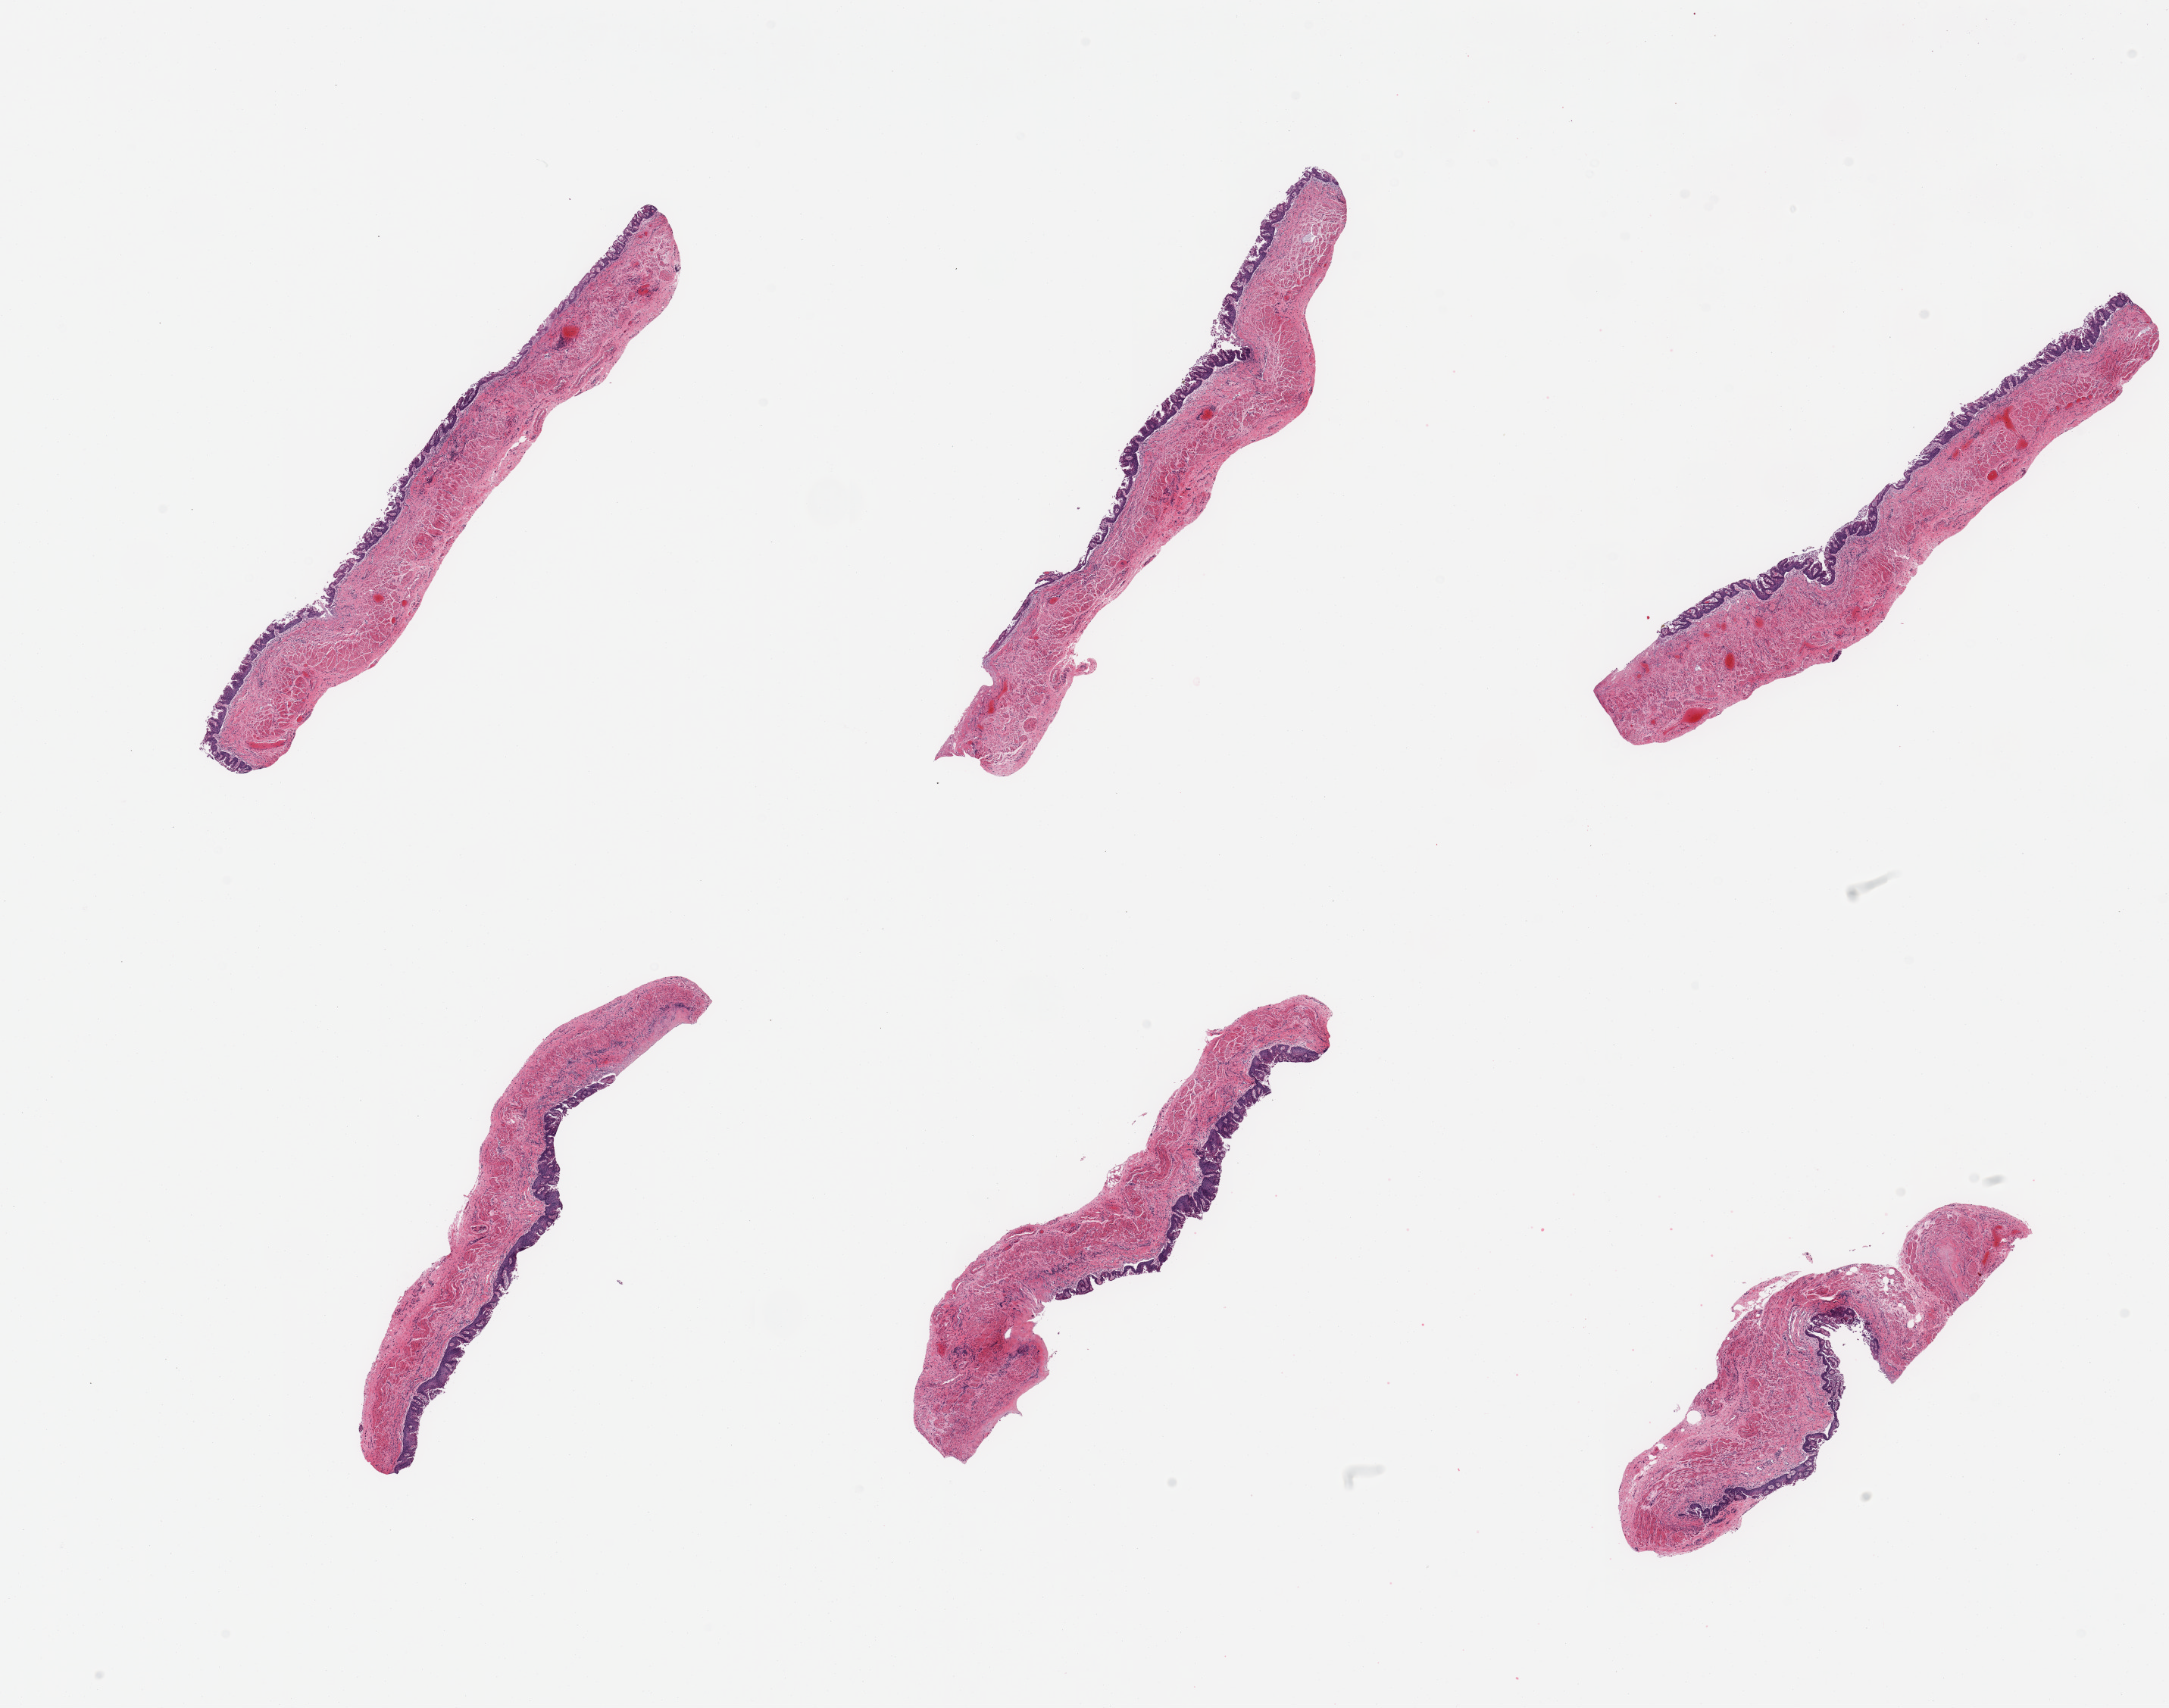
Hematoxylin and eosin (H&E) whole-slide image — a low-resolution overview of the entire scanned area, about 22.6 x 17.8 mm, PAXgene-fixed, paraffin-embedded tissue, target tissue: esophageal mucous membrane, donor tissue sample.
Pathologist's review note for this sample: 6 pieces; moderate epithelial sloughing.